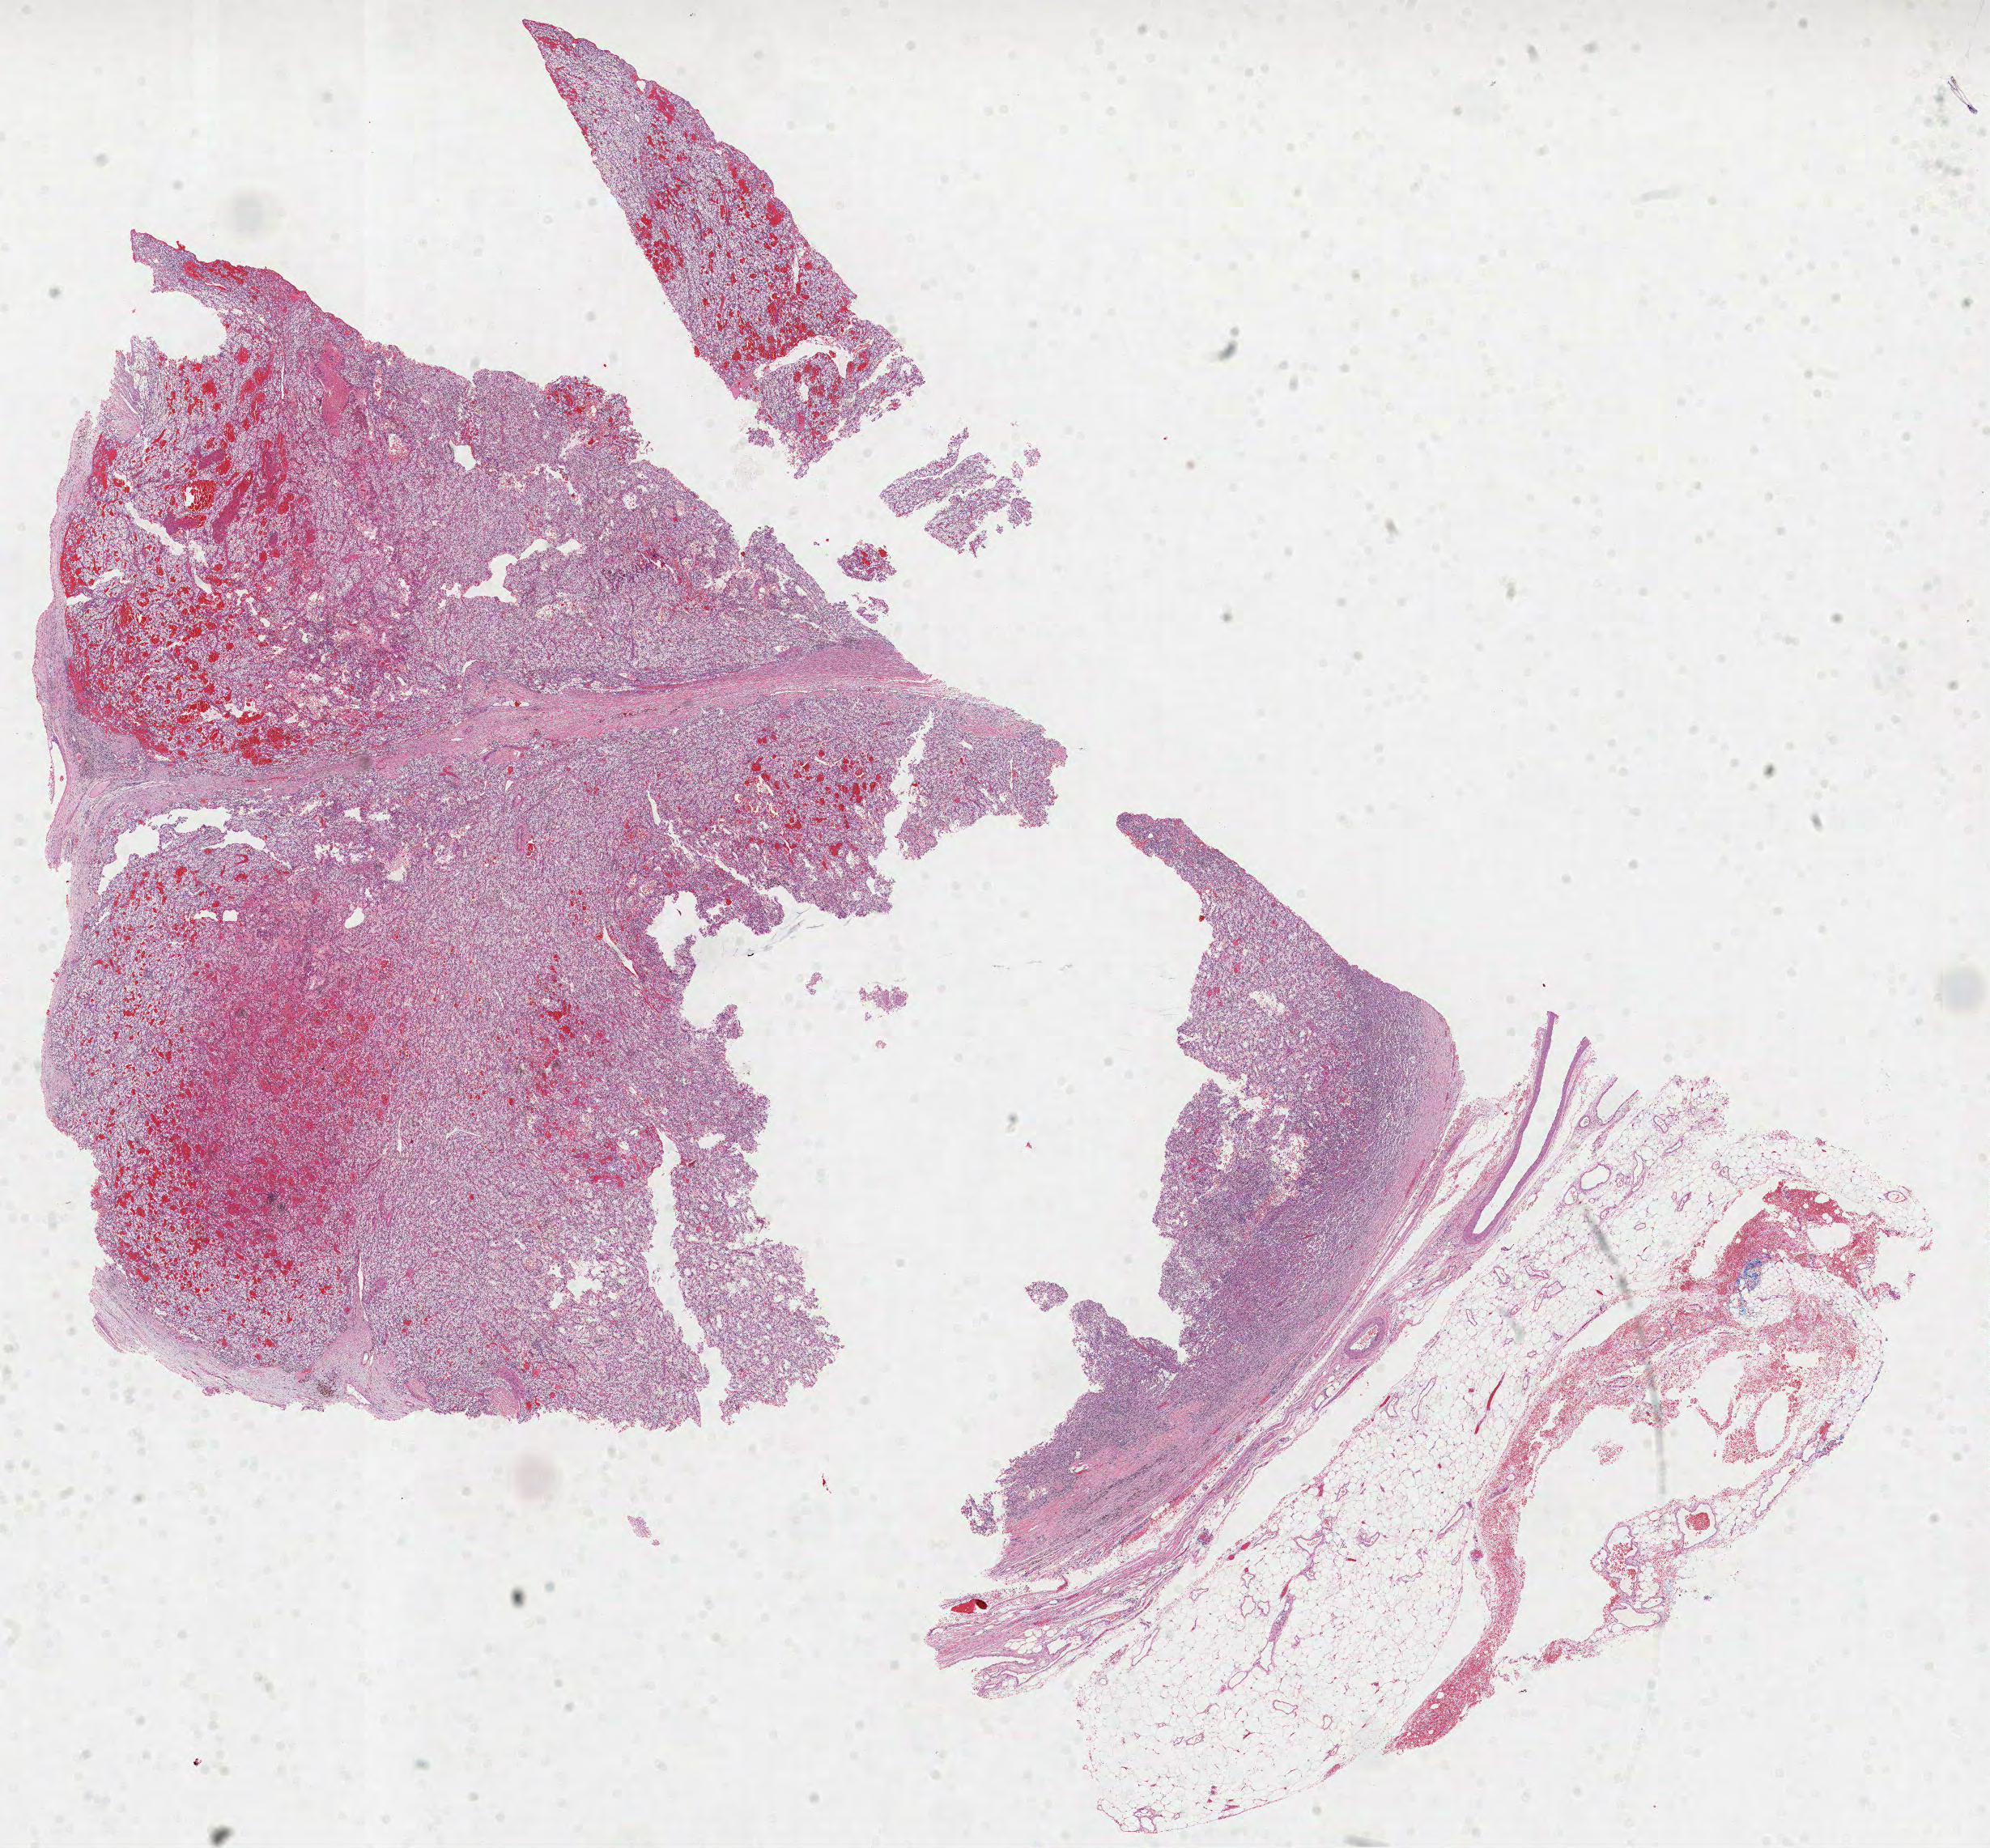
Digitized H&E tissue section (whole slide) — whole scanned area (about 19.8 x 18.4 mm, from a 40x scan) shown as a low-resolution overview. FFPE section. Sample: primary tumour, kidney. Male, age 78 years at initial diagnosis. Histologic grade: G4 (undifferentiated).
Pathologic diagnosis: Clear cell adenocarcinoma, NOS. AJCC pathologic stage: II. Laterality: right.